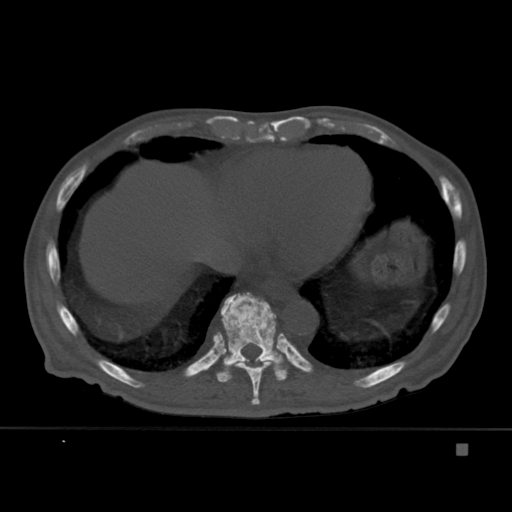
CT including the spine, one axial slice. Position 239 of 451 along the scan axis. Bone window (W 1800 / L 400 HU). 1.5 mm slice thickness. 512 × 512 image matrix. Male patient, age 75 years. Case-level facts recorded for this patient, not image findings: primary cancer: prostate.
Annotated regions visible in this slice (semi-automatic segmentation, software-assisted and operator-edited):
- T10 vertebra: bounding box (x1, y1, x2, y2) in pixels: (216, 292, 288, 383)
- T9 vertebra: (223, 334, 280, 405)